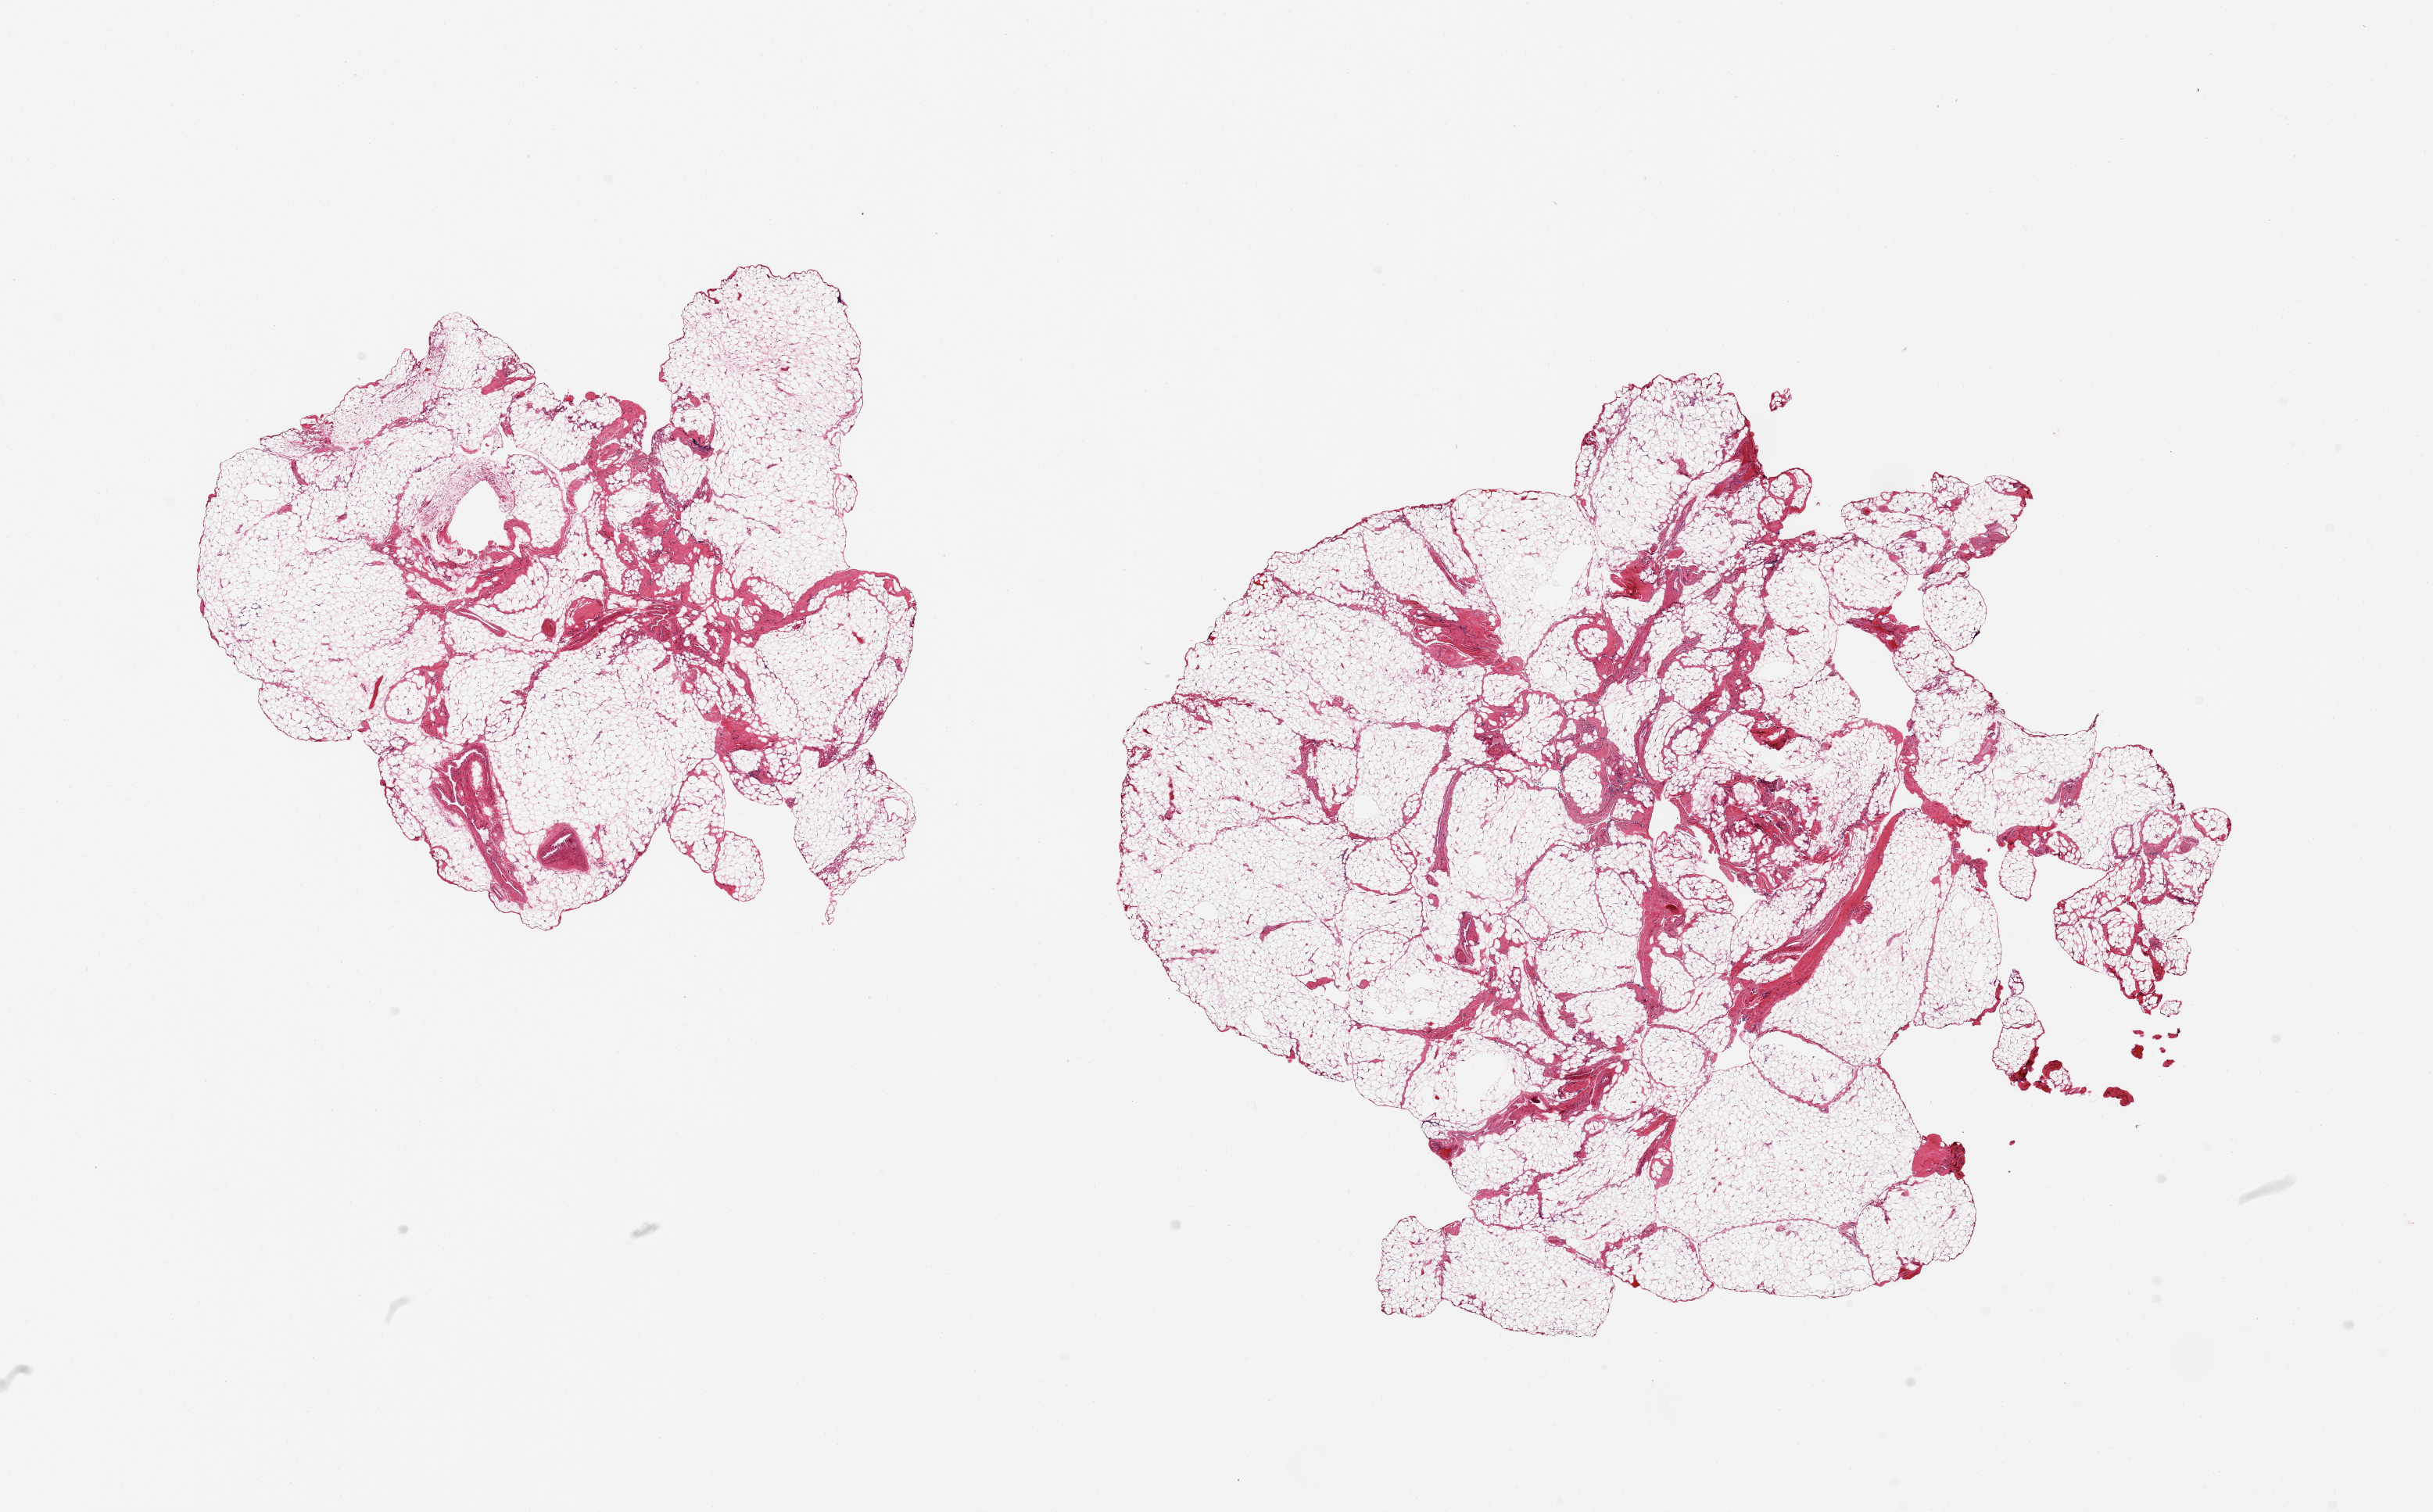
Whole-slide image, hematoxylin and eosin (H&E) stain, whole scanned area (about 24.6 x 15.3 mm, acquisition: 20x scan) shown as a low-resolution overview. PAXgene-fixed, paraffin-embedded tissue. Target tissue: omentum. Tissue donor sample. Donor: male.
Reviewer comment on this tissue sample: 2 pieces; 10-20% fibrous/vessels.